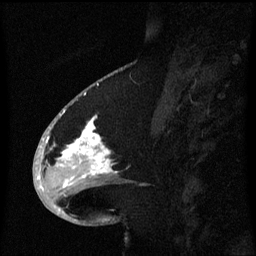
Breast MRI (dynamic contrast-enhanced), one sagittal slice. Slice 28 of 60 in the series (ordered by position). Dynamic contrast-enhanced series, image 2 of 3 at this slice position (ordered by acquisition). 1.5 T. TE 4.2 ms, TR 8.4 ms. 256 × 256 image matrix. Patient: female, 53 years. From the clinical record (not read from this slice): setting: breast cancer imaged before/during neoadjuvant chemotherapy; receptor status: HR-positive, HER2-negative.
Annotated regions visible in this slice (semi-automatically segmented with operator editing):
- analysis volume of interest (the breast-tissue region the enhancement analysis was run in; not a lesion): bounding box (x1, y1, x2, y2) in pixels: (49, 108, 125, 201)
- tumour enhancement mask (voxels above the 70 % enhancement threshold inside the analysis volume of interest): (49, 116, 113, 177)